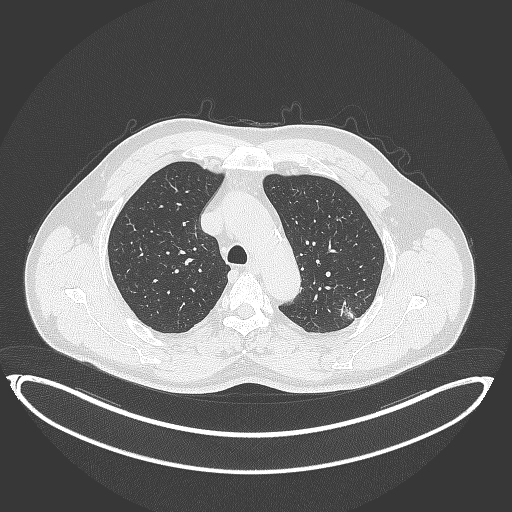
Chest CT, one axial slice; slice 272 of 399 in the series (ordered by position); lung window (W 1500 / L -600 HU); 1 mm slice thickness; 512 × 512 image matrix. Patient: male, 58 years. Case-level facts recorded for this patient, not image findings: clinical TNM (as recorded): T1c N0 M0.
Structures marked on this image (rectangle marked by the reading radiologist):
- lung tumour (recorded histology: adenocarcinoma): box from (x=335, y=295) to (x=358, y=322) px